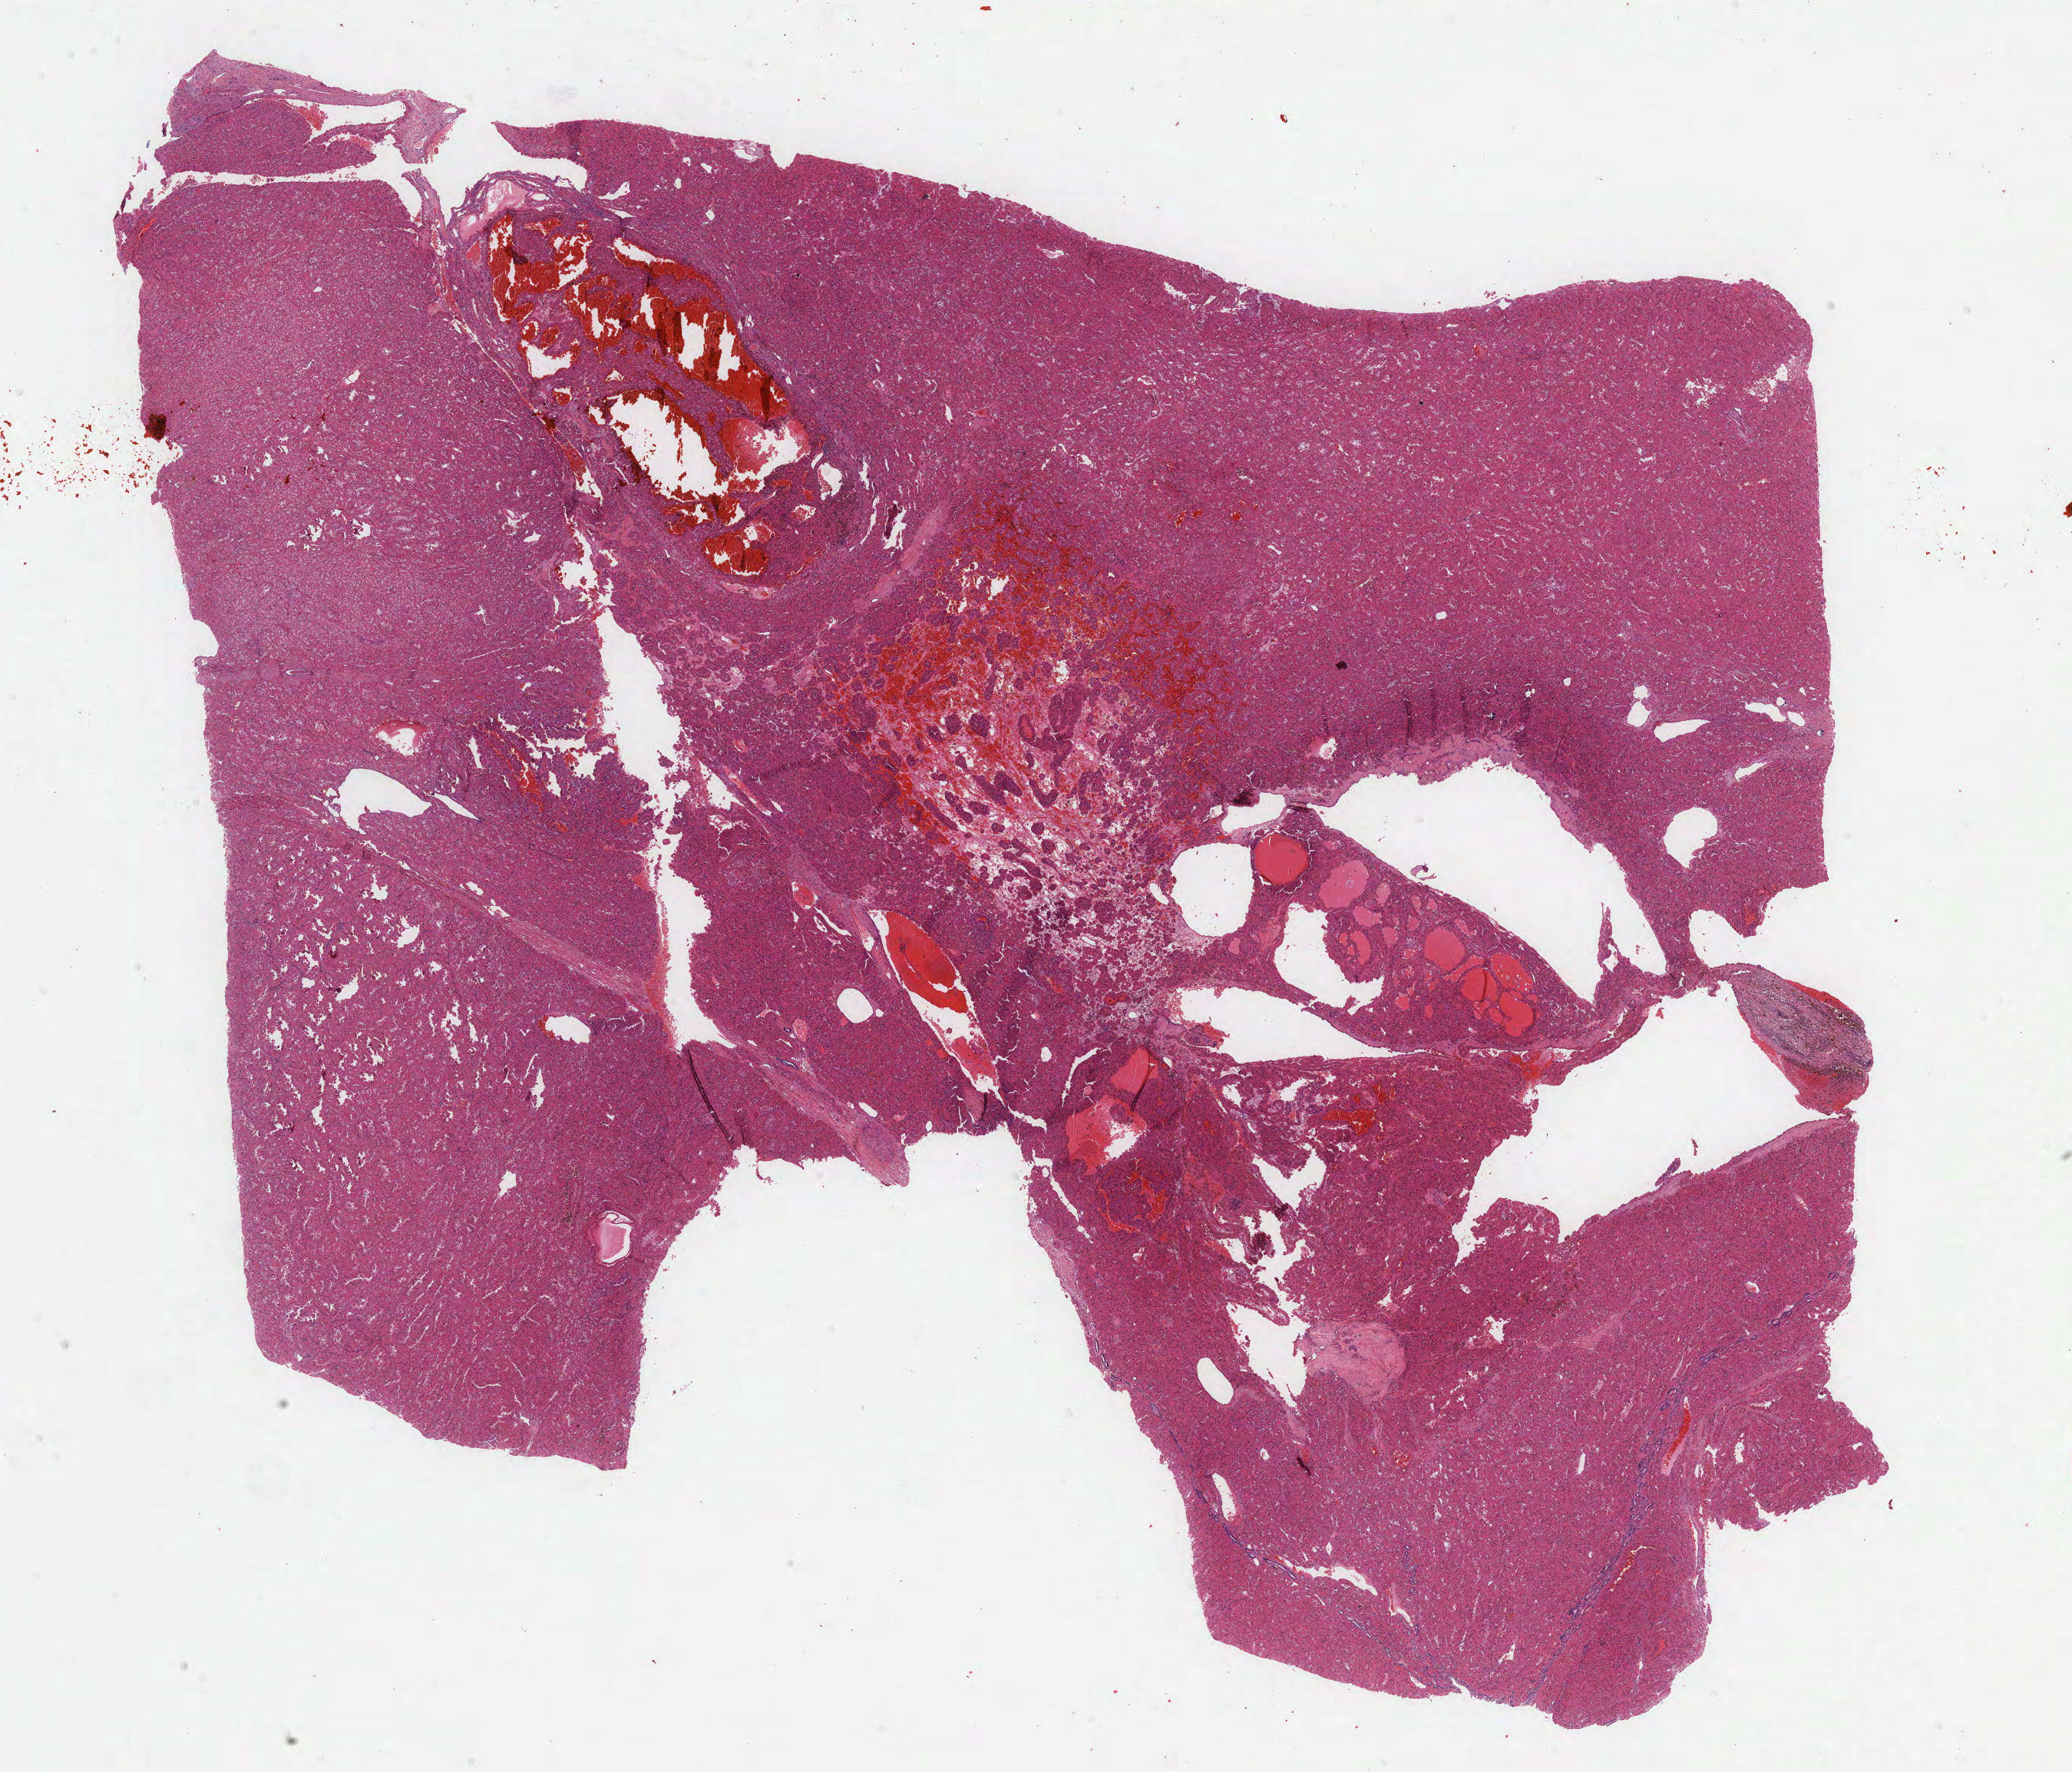
Whole-slide histology image, H&E-stained, whole scanned area (about 21.8 x 18.6 mm) shown as a low-resolution overview; FFPE section; kidney, primary tumour sample. Patient: female, age at initial diagnosis 56 years.
TNM: T1b N0 MX. Laterality: right. AJCC pathologic stage: I (7th edition). Diagnosis: Papillary adenocarcinoma, NOS.